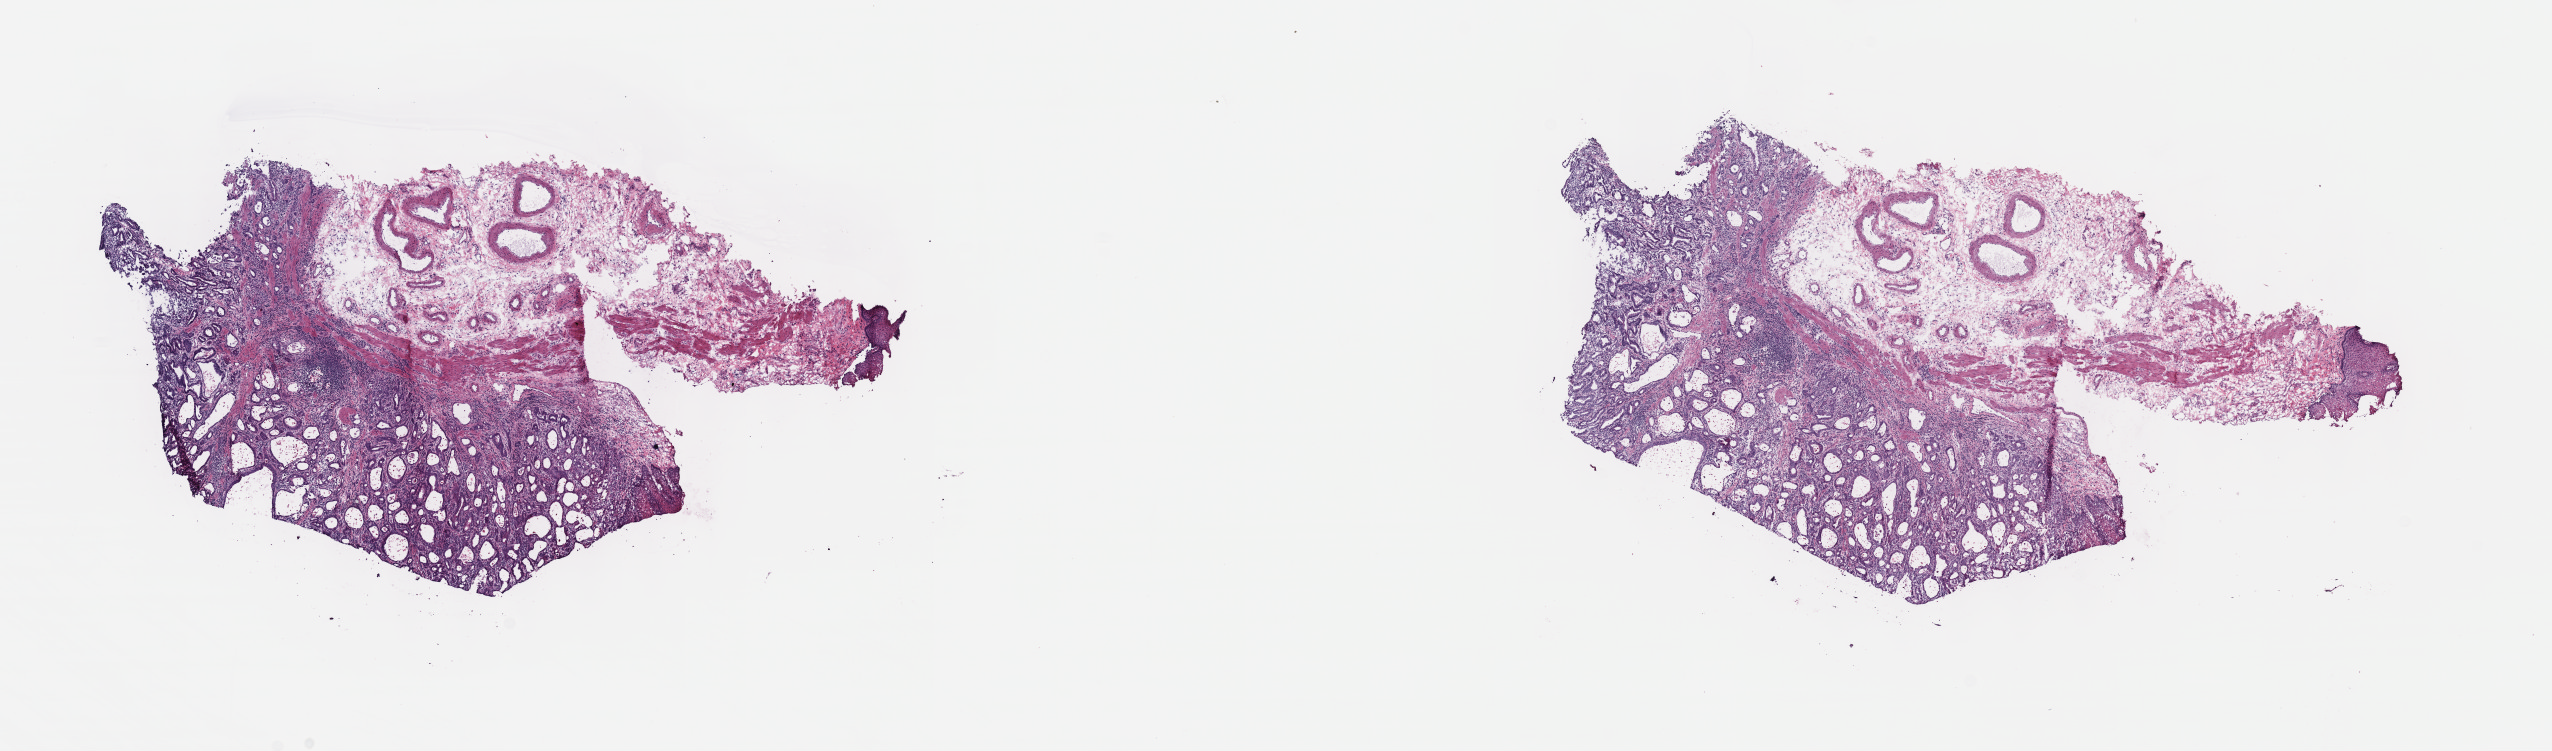
Digitized H&E tissue section (whole slide), shown as a low-resolution overview of the whole scanned area (about 20.6 x 6.1 mm). Frozen section from the top of the tissue portion. Sample: primary tumour, esophagus. Male, age 86 years at initial diagnosis. Histologic grade: GX (grade cannot be assessed). Pathologist review of this section (percent, as recorded): tumour cells 60%, tumour nuclei 60%, normal cells 40%, stromal cells 0%, necrosis 0%. Inflammatory infiltration, as recorded: lymphocyte infiltration 10%, monocyte infiltration 0%, neutrophil infiltration 1%.
AJCC pathologic stage: IIB (7th edition). Pathologic diagnosis: Adenocarcinoma, NOS (lower third of esophagus). Lymph nodes positive (case pathology): 2 of 11 examined.